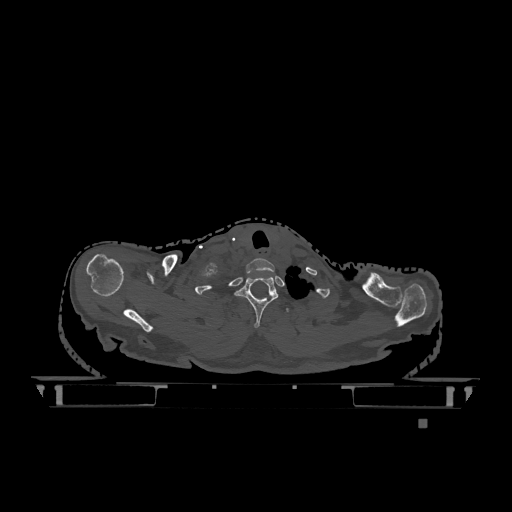
CT including the spine, one axial slice; position 998 of 1317 along the scan axis; bone window (W 1800 / L 400 HU); 0.5 mm slice thickness; 512 × 512 image matrix, field of view 500 × 500 mm. Female patient, age 74 years. Case-level facts recorded for this patient, not image findings: primary cancer: lung; vertebrae with lytic lesions (as recorded): T1, T4, T5, T6, L4, L5.
Annotated regions visible in this slice (semi-automatic segmentation, software-assisted and operator-edited):
- T1 vertebra: box from (x=235, y=276) to (x=278, y=328) px
- T2 vertebra: (x=286, y=308)–(x=289, y=312)